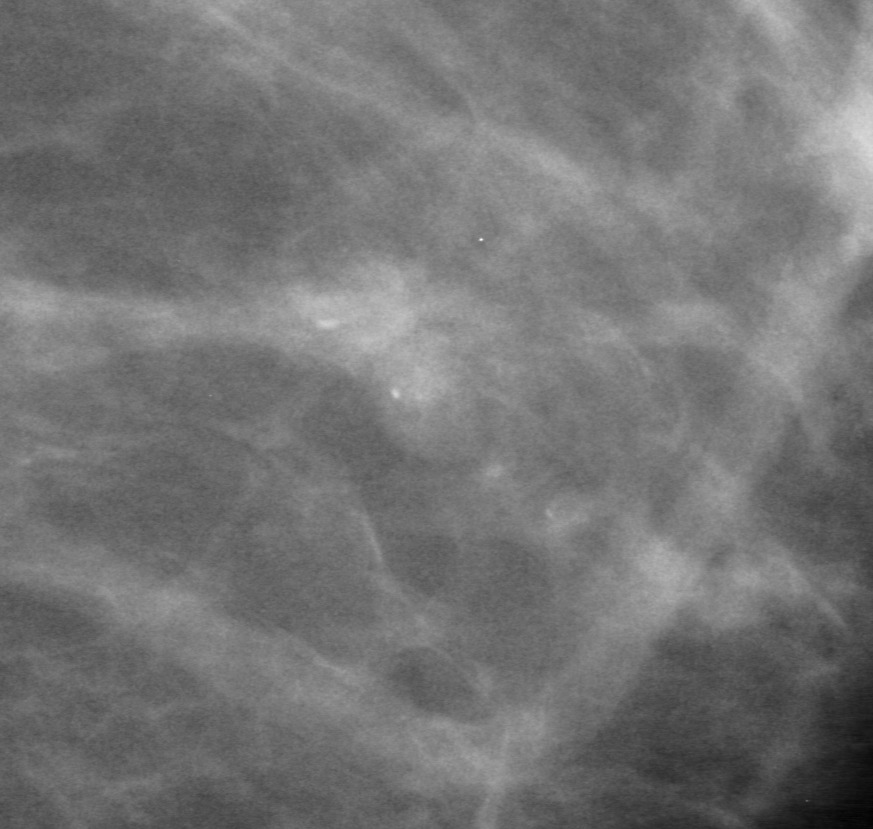
Cropped region of a digitized screen-film mammogram centred on a radiologist-marked abnormality; left breast; MLO view.
Calcifications, morphology fine linear branching, distribution clustered; BI-RADS assessment category 3; pathology result (as recorded, not read from the image): malignant.